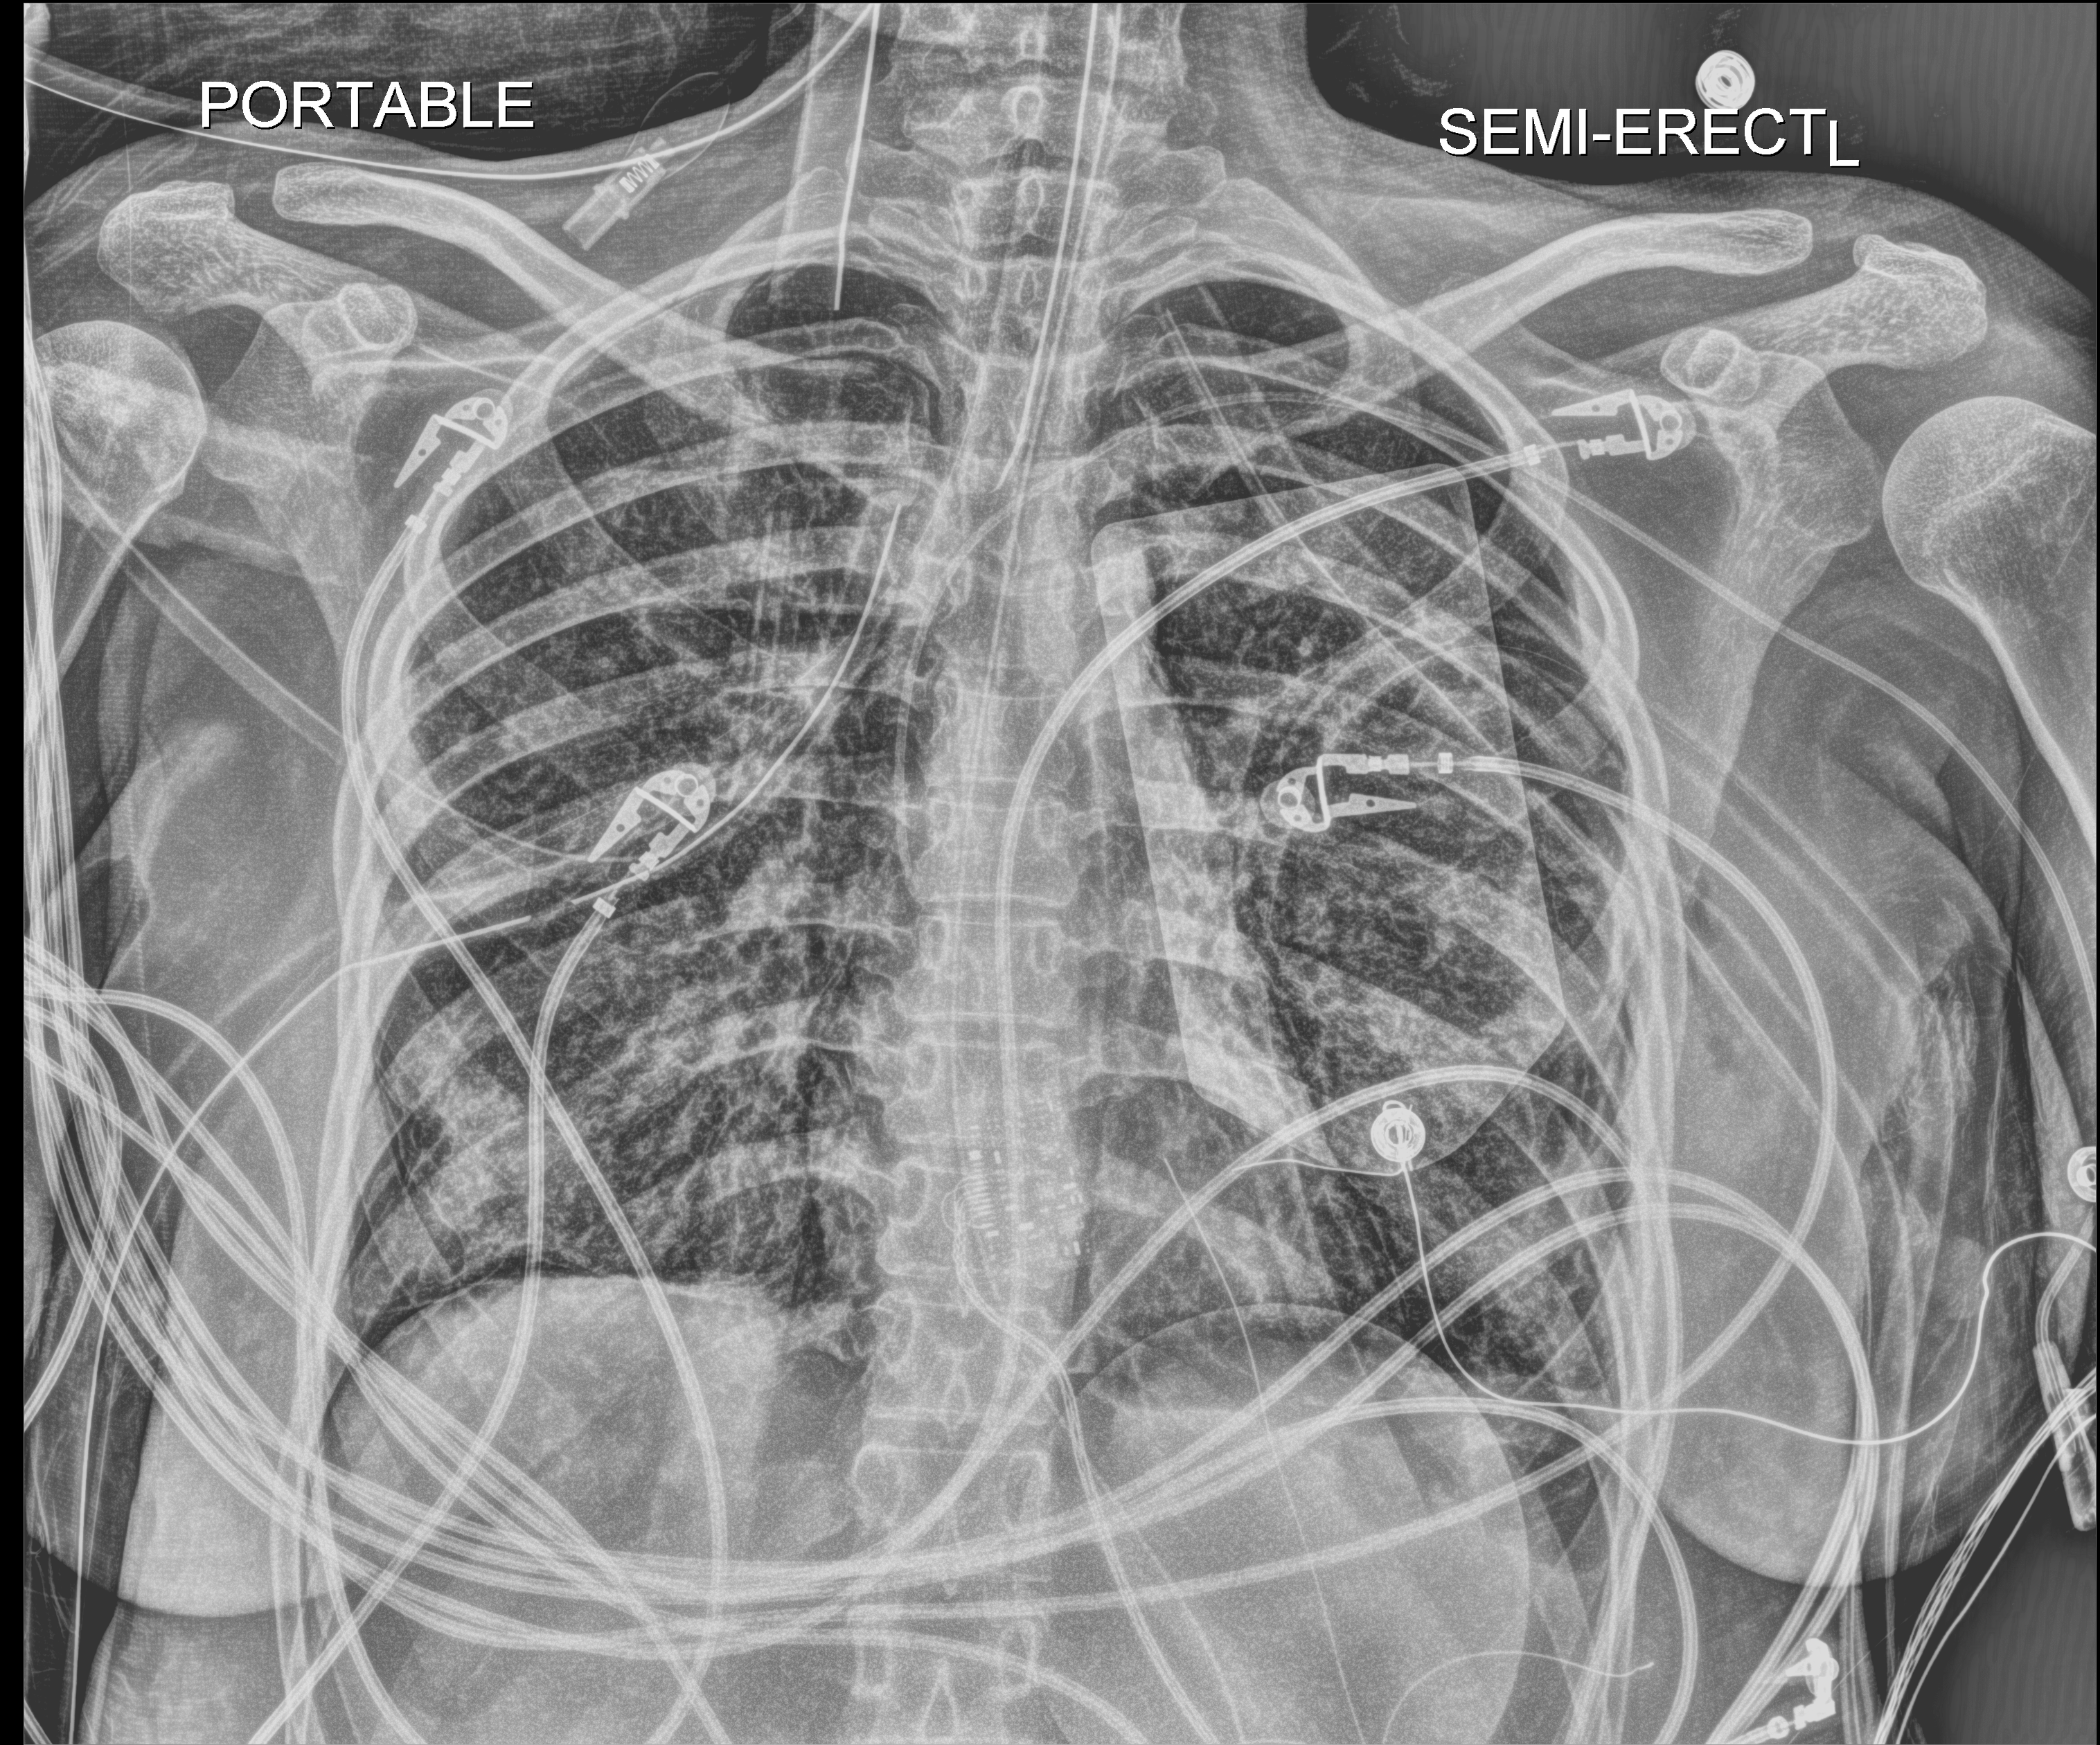
Chest X-ray (portable). Patient hospitalised with COVID-19, aged 18–59 years.
Hospital-stay facts (about this admission, not read from this image; timing relative to this image not recorded): hypertension (admission record): no.